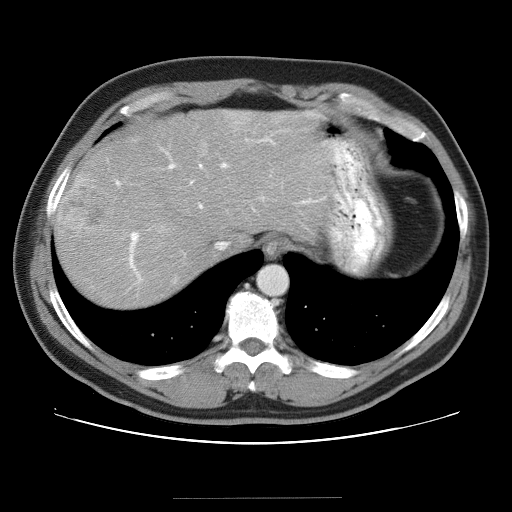
Contrast-enhanced abdominal CT (liver protocol), one axial slice. Slice 30 of 40 in the series (ordered by position). 120 kVp. Soft-tissue window (W 400 / L 40 HU). 5 mm slice thickness. 512 × 512 image matrix. Case-level facts recorded for this patient, not image findings: diagnosis: hepatocellular carcinoma (patient treated with transarterial chemoembolisation; whether this scan precedes or follows treatment is not stated here); TNM stage (as recorded): Stage-IVA; Child-Pugh class: B; tumour nodularity: multinodular.
Outlined on this slice (semi-automatic segmentation, software-assisted and operator-edited):
- abdominal aorta: bounding box [x1, y1, x2, y2] px = [258, 266, 287, 295]
- liver parenchyma outside the tumour (the mass and vessels are separate outlines, so this box may not span the whole liver): [54, 110, 336, 306]
- mass: [58, 179, 116, 240]
- liver vessels: [116, 138, 325, 281]